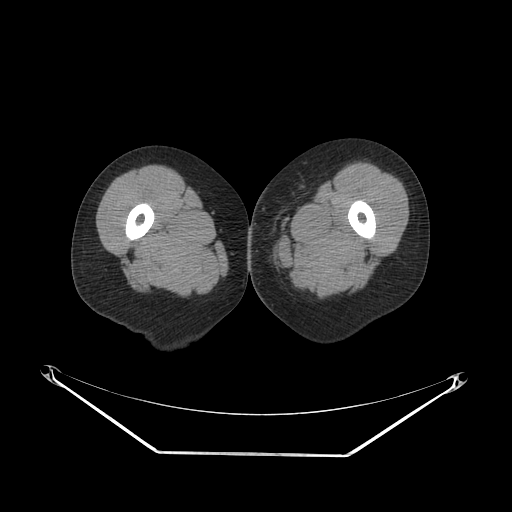
CT of an extremity soft-tissue mass (from a PET/CT study), one axial slice; reconstruction kernel SOFT; 140 kVp; soft-tissue window (W 400 / L 40 HU); 3.75 mm slice thickness; 512 × 512 image matrix. Female patient. Case-level facts recorded for this patient, not image findings: histological type: leiomyosarcoma; grade: high; site of the primary tumour: groin.
Structures marked on this image (expert contour drawn on MRI and transferred to this co-registered scan by the dataset authors):
- gross tumour volume including surrounding oedema: bounding box [x1, y1, x2, y2] px = [249, 221, 277, 247]